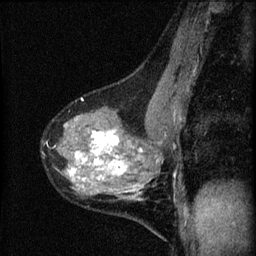
Breast MRI (dynamic contrast-enhanced), one sagittal slice. Slice 34 of 60 in the series (ordered by position). Dynamic contrast-enhanced series, image 2 of 4 at this slice position (ordered by acquisition). 1.5 T. TE 4.2 ms, TR 8.2 ms. 256 × 256 image matrix. Female patient, age 41 years.
Structures marked on this image (semi-automatically segmented with operator editing):
- analysis volume of interest (the breast-tissue region the enhancement analysis was run in; not a lesion): bounding box <42,91,166,200> (left, top, right, bottom; pixels)
- tumour enhancement mask (voxels above the 70 % enhancement threshold inside the analysis volume of interest): <68,131,143,200>